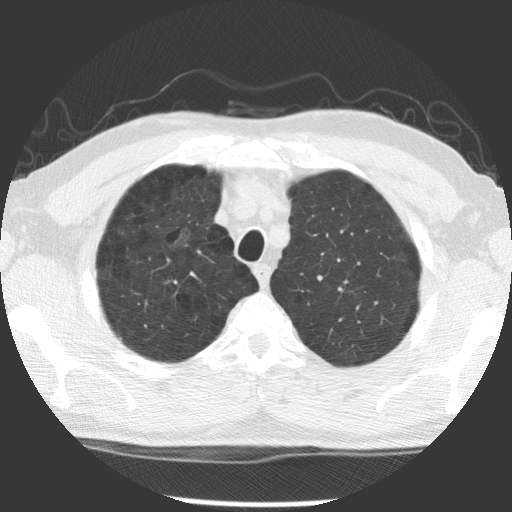
Low-dose screening chest CT, axial slice; first (baseline) screen; lung window (W 1500 / L -600 HU); slice 95 of 122 in the series; 512 × 512 image matrix, field of view 350 × 350 mm. Male participant, aged 60 years at enrolment. Former smoker at enrolment.
Expert reader's lesion annotation, box from (x=142, y=217) to (x=197, y=264) px. The exam's reader record, not a measurement of the box and not confirmed to be the same lesion: non-calcified nodule or mass ≥4 mm, right middle lobe, 20 × 20 mm, poorly defined margins, ground glass attenuation. Later outcome: lung cancer diagnosed 863 days after this screen (after the third annual screen) — papillary adenocarcinoma, NOS, right upper lobe, moderately differentiated (G2), stage IB (AJCC 6th edition), 32 mm at pathology.